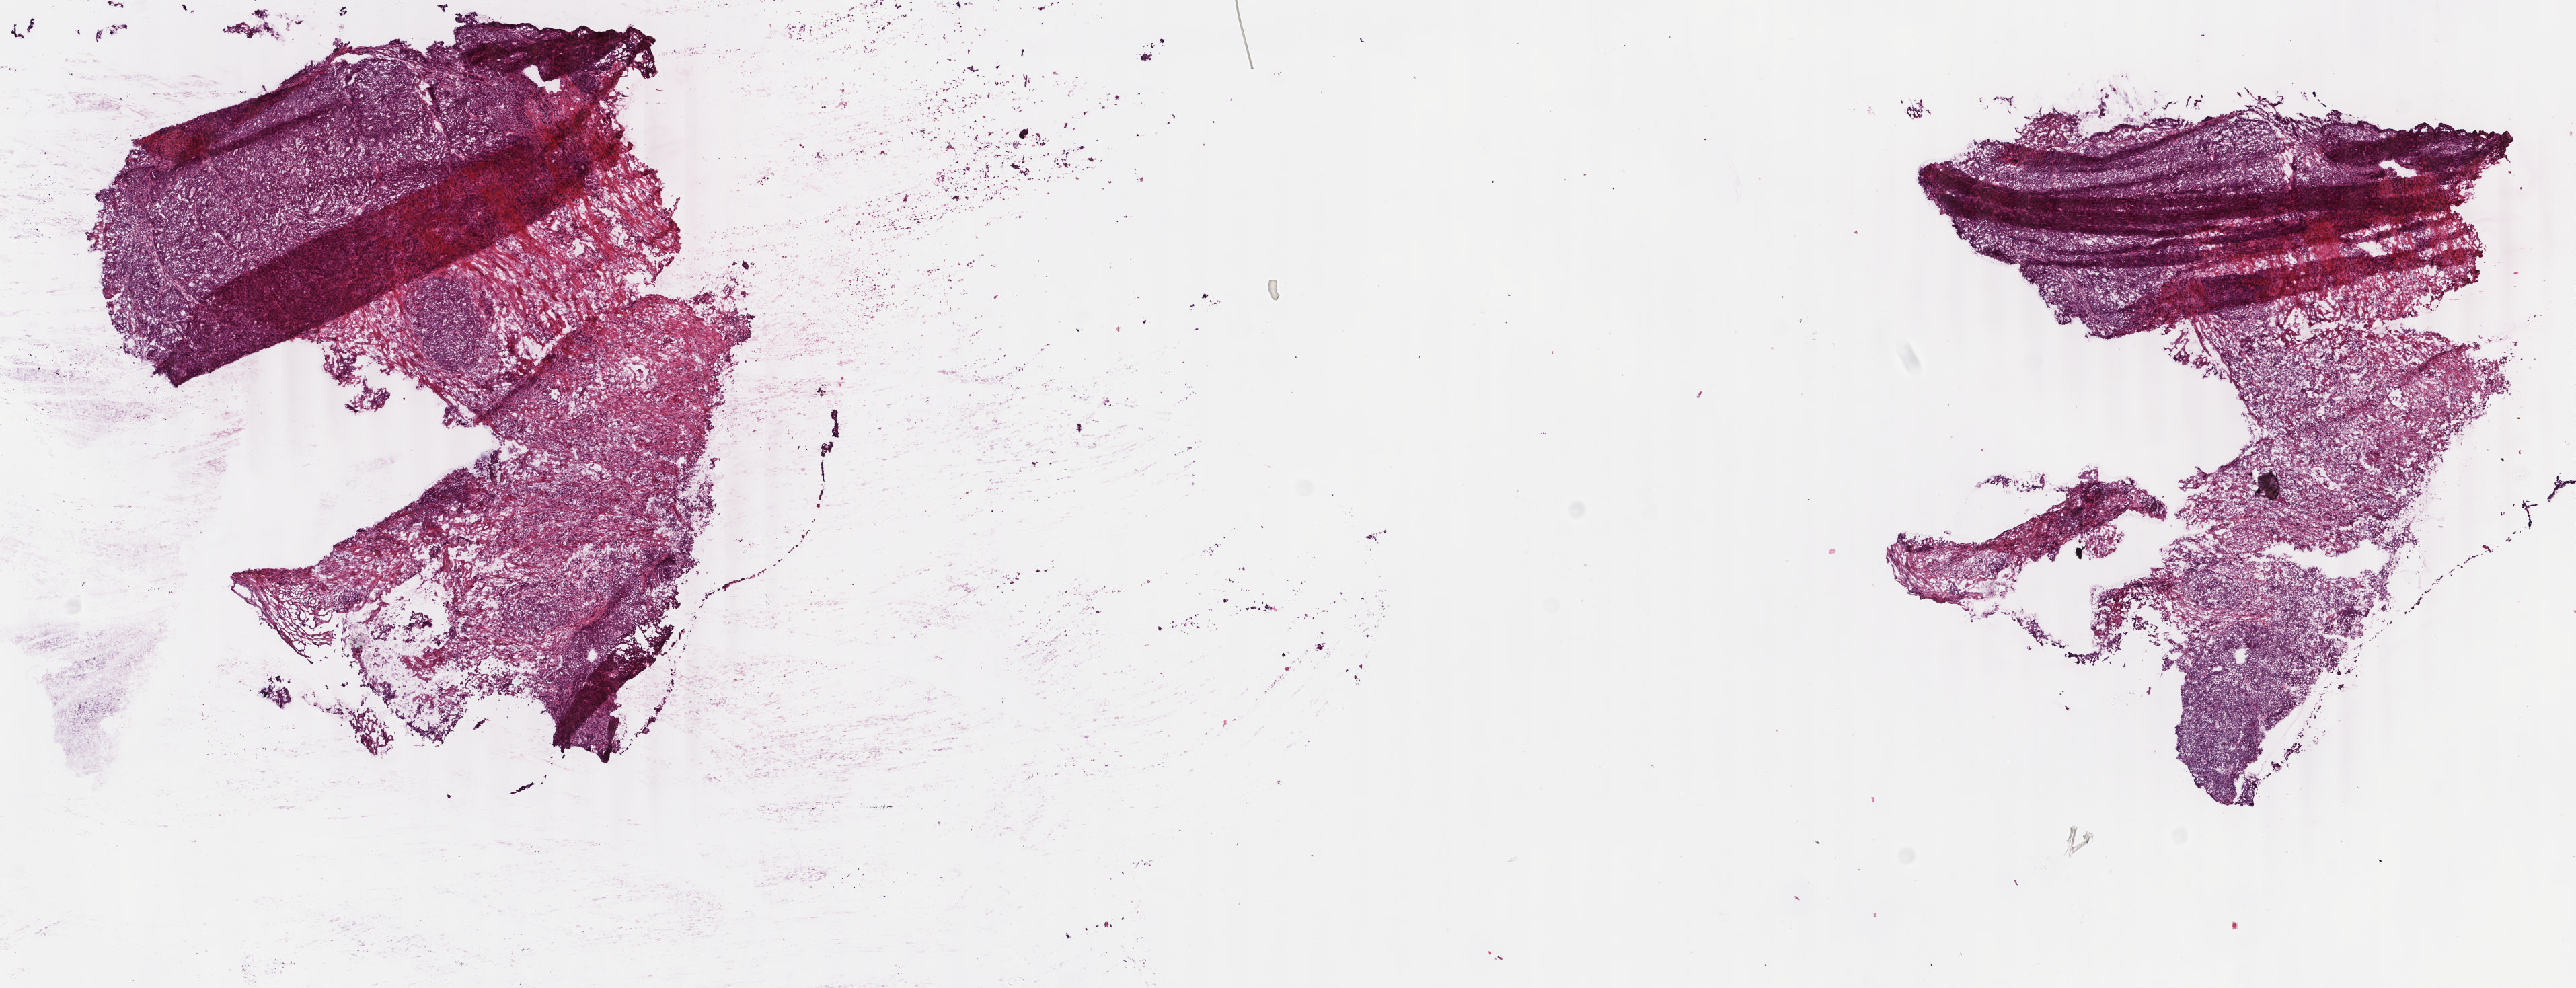
Whole-slide histology image, H&E-stained, shown as a low-resolution overview of the whole scanned area (about 15.2 x 5.8 mm). Frozen section. Sample: primary tumour, colon. Patient: female, age at initial diagnosis 46 years. Slide review estimates, as recorded: tumour cells 75%, tumour nuclei 75%, normal cells 0%, stromal cells 24%, necrosis 1%. Infiltration values recorded for this section: lymphocyte infiltration 17%, monocyte infiltration 3%, neutrophil infiltration 0%.
- diagnosis: Adenocarcinoma, NOS (transverse colon)
- AJCC pathologic stage: IIB (6th edition)
- lymph nodes positive (case pathology): 0 of 45 examined